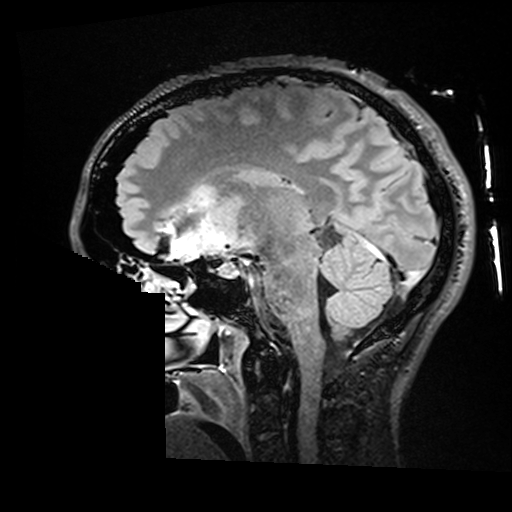
Brain MRI from a brain-tumour surgery series, one sagittal slice; position 92 of 176 along the scan axis; T2 FLAIR; 1 mm slice thickness; 512 × 512 image matrix, field of view 250 × 250 mm. Case-level facts recorded for this patient, not image findings: histopathology: Astrocytoma; WHO grade: 2; IDH mutation: yes.
Annotated regions visible in this slice (expert manual segmentation):
- residual tumour: bounding box (x1, y1, x2, y2) in pixels: (204, 194, 213, 201)